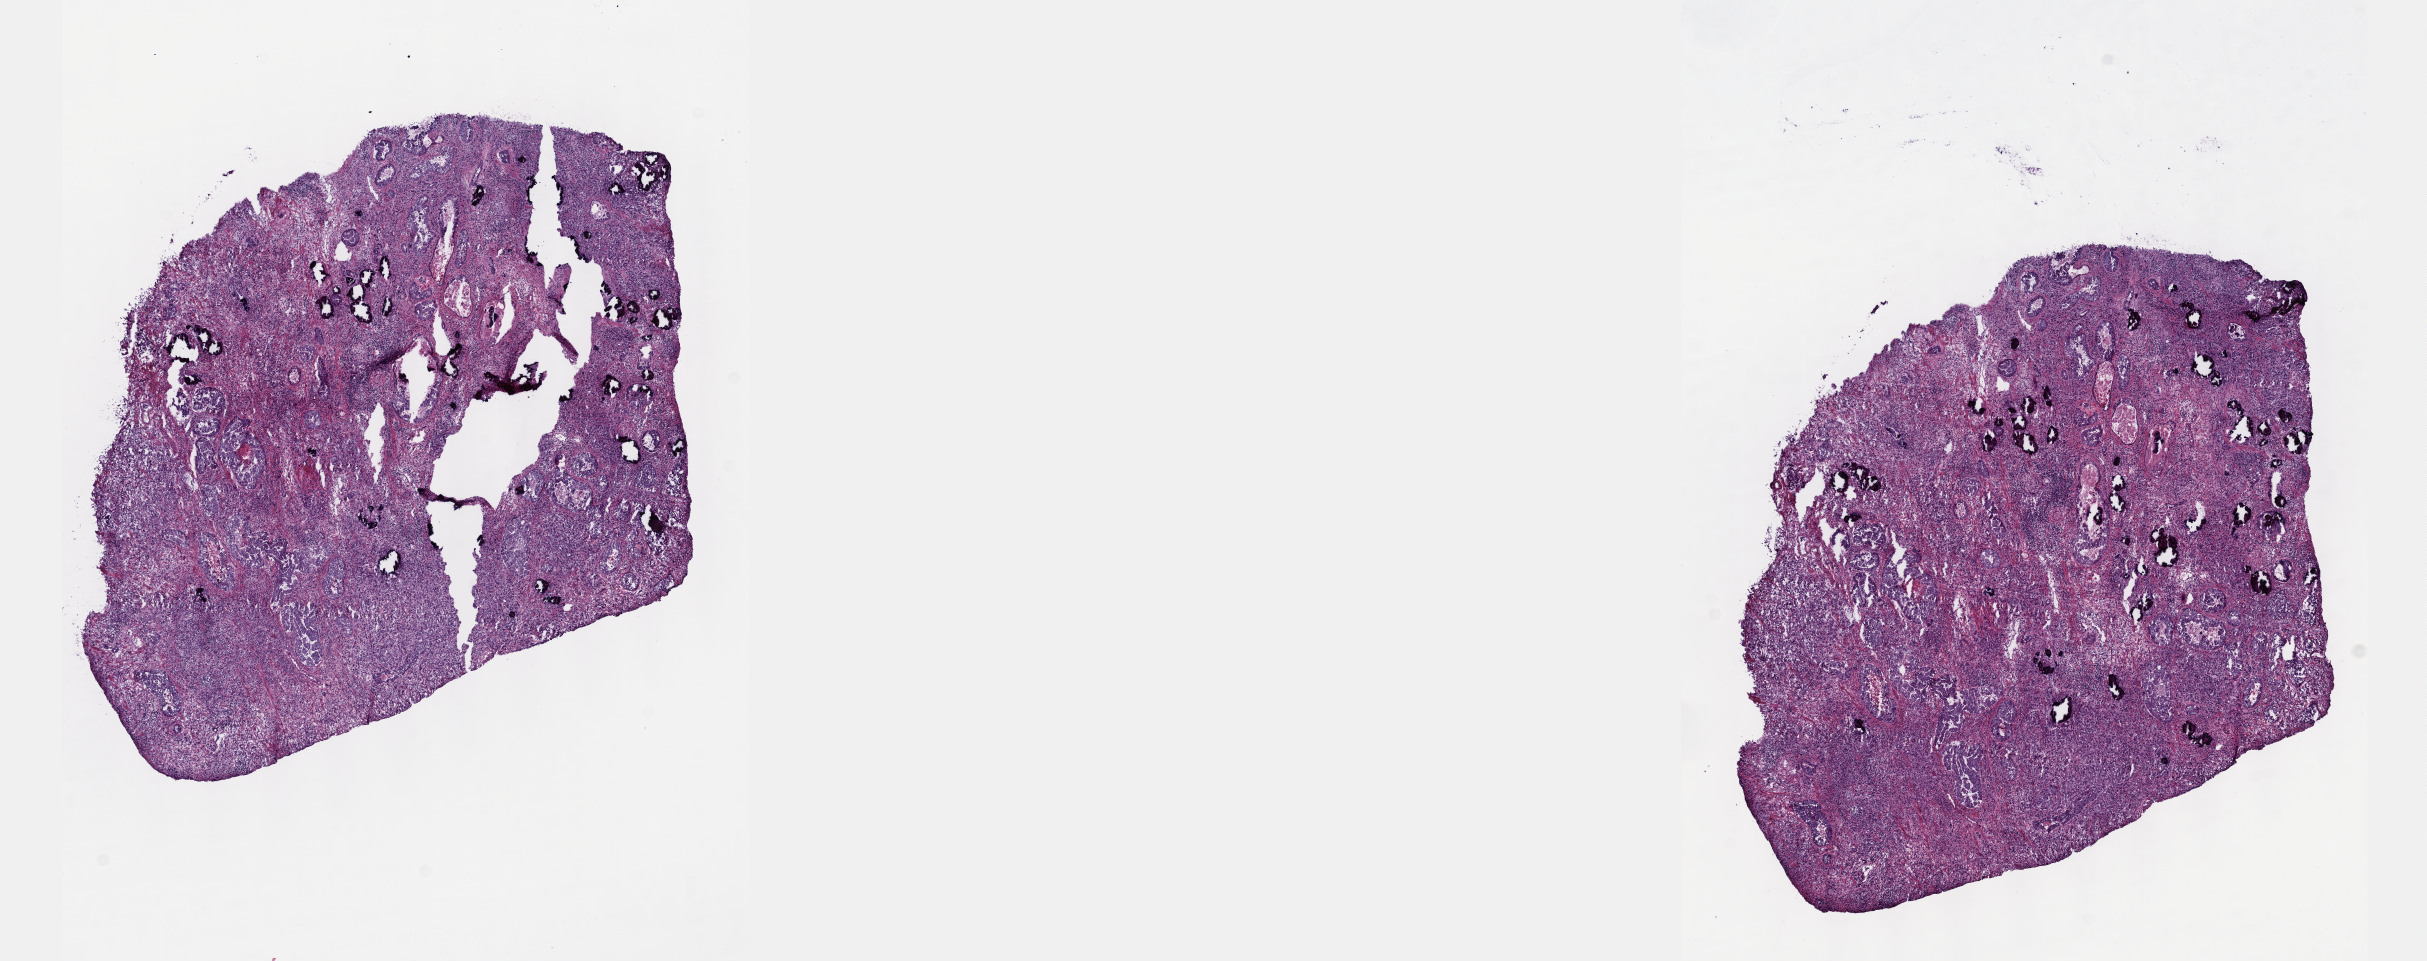
Digitized H&E tissue section (whole slide), low-resolution overview of the scanned area, about 19.6 x 7.8 mm (from a 40x scan); frozen section from the top of the tissue portion; sample: primary tumour, prostate. Patient: male, age at initial diagnosis 63 years. Gleason score: 10 (5+5). Composition of this section per pathologist review: tumour cells 50%, tumour nuclei 60%, normal cells 10%, stromal cells 40%, necrosis 0%. Inflammatory infiltration, as recorded: lymphocyte infiltration 90%, monocyte infiltration 10%, neutrophil infiltration 0%.
Histologic diagnosis: Adenocarcinoma, NOS (prostate gland). Lymph nodes positive (case pathology): 2 of 18 examined.